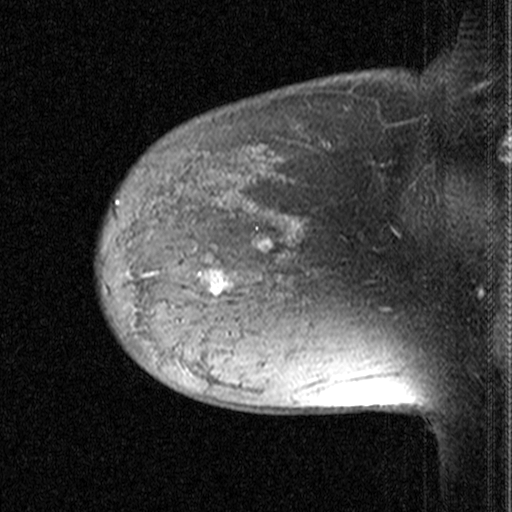
Breast MRI (dynamic contrast-enhanced), one sagittal slice; slice 33 of 44 in the series (ordered by position); dynamic contrast-enhanced study with each time point stored as its own series, time point 2 of 3 at this slice position (early post-contrast, ordered by acquisition time); 1.5 T; TE 4.5 ms, TR 11 ms; 512 × 512 image matrix, field of view 200 × 200 mm. Female patient, age 38 years. From the clinical record (not read from this slice): setting: breast cancer imaged before/during neoadjuvant chemotherapy; receptor status: HR-positive, HER2-negative.
Structures marked on this image (semi-automatic segmentation, software-assisted and operator-edited):
- analysis volume of interest (the breast-tissue region the enhancement analysis was run in; not a lesion): box from (x=170, y=232) to (x=259, y=331) px
- tumour enhancement mask (voxels above the 90 % enhancement threshold inside the analysis volume of interest): (x=211, y=272)–(x=228, y=294)